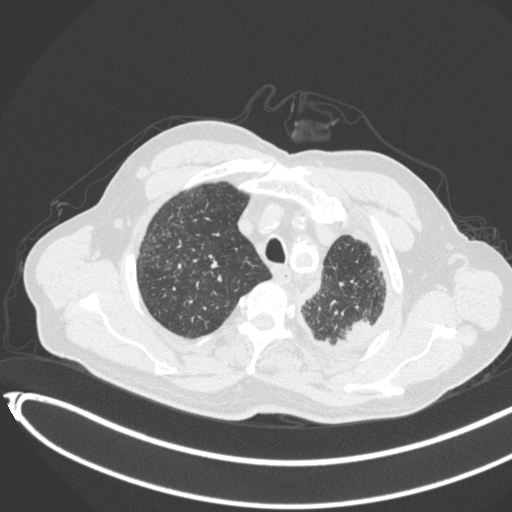
Chest CT, one axial slice. Position 359 of 451 along the scan axis. Reconstruction kernel B31f. Lung window (W 1500 / L -600 HU). 512 × 512 image matrix. Patient: male, 78 years. From the clinical record (not read from this slice): clinical TNM (as recorded): T1c N0 M1.
Outlined on this slice (rectangle marked by the reading radiologist):
- lung tumour (recorded histology: adenocarcinoma): bounding box (x1, y1, x2, y2) in pixels: (338, 313, 373, 342)